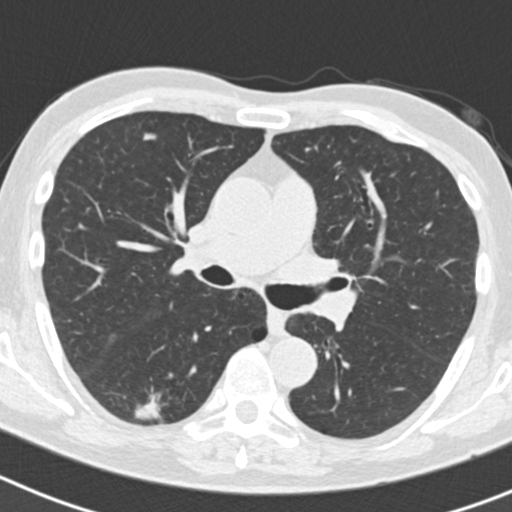
Chest CT (low-dose screening protocol), one axial image, second annual screen, lung window (W 1500 / L -600 HU), 2 mm slice thickness, 120 kVp. Male, age 70 years at enrolment. Current smoker at enrolment.
Expert reader's lesion annotation, bounding box (x1, y1, x2, y2) in pixels: (134, 379, 195, 434). The screening reader recorded 5 non-calcified nodules or masses ≥4 mm on this exam (right lower lobe, right lower lobe, right upper lobe, right upper lobe, left upper lobe); which of them this box marks is not recorded. Lung cancer was diagnosed 622 days after this screen (after the third annual screen): bronchiolo-alveolar adenocarcinoma, NOS, right lower lobe, poorly differentiated (G3), stage IB (AJCC 6th edition), 30 mm at pathology.